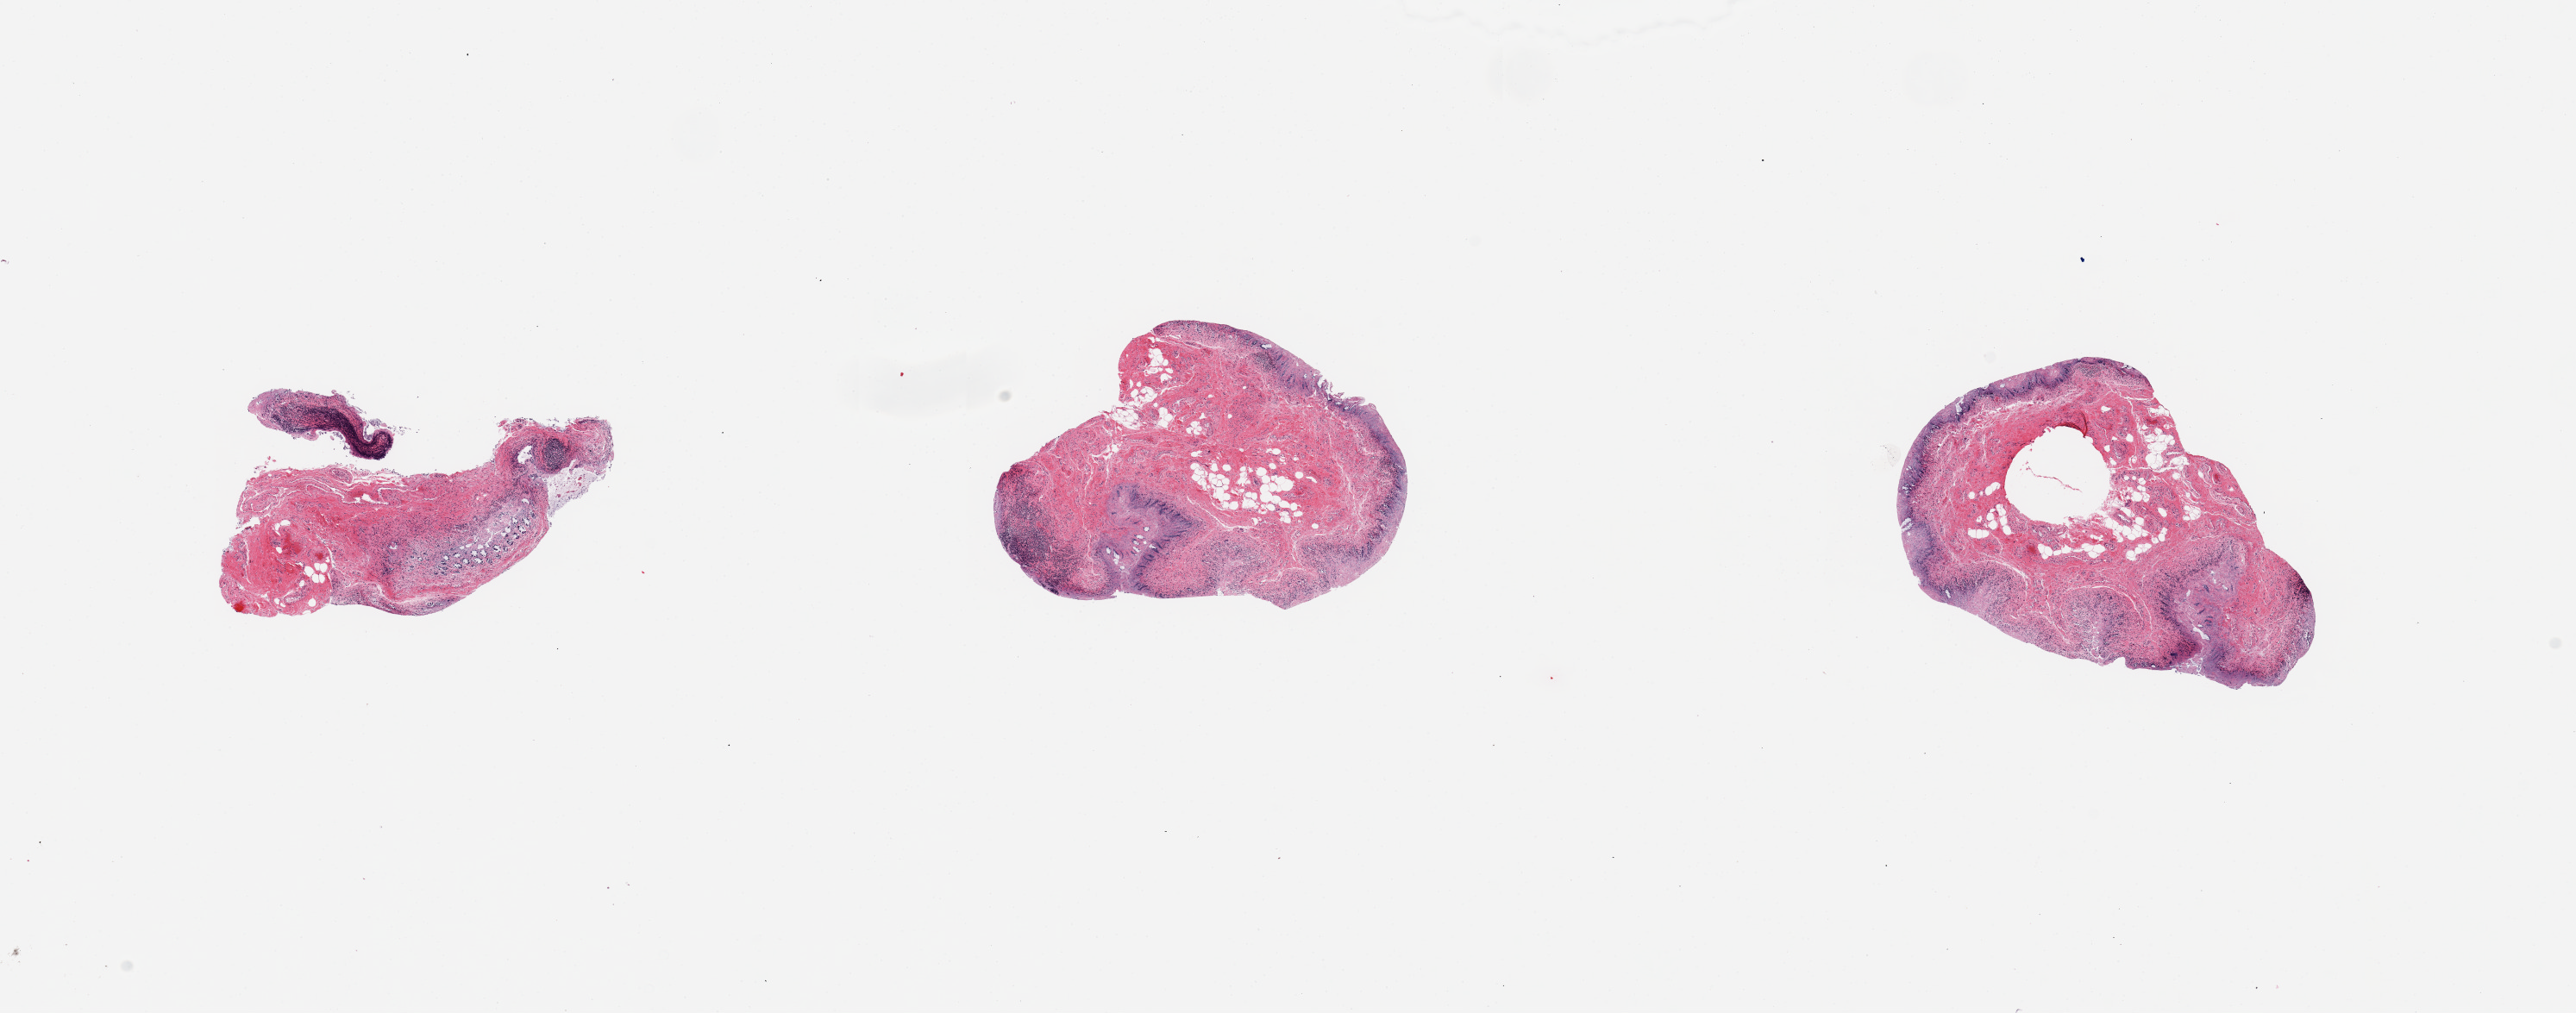
Digitized haematoxylin and eosin-stained section — whole scanned area (about 23.6 x 9.3 mm, from a 20x scan) shown as a low-resolution overview, PAXgene-fixed, paraffin-embedded tissue, sampled site (target tissue): ileum, tissue donor sample.
• pathologist's review note for this sample: 3 pieces, mucosa autolyzed completely; ~5-10% residual lymphoid aggregates